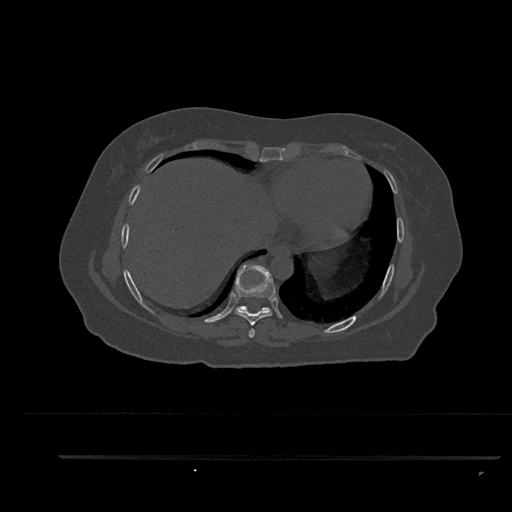
CT including the spine, one axial slice; position 449 of 797 along the scan axis; reconstruction kernel Br40s/3; 120 kVp; bone window (W 1800 / L 400 HU); 0.5 mm slice thickness; 512 × 512 image matrix. Patient: female, 44 years. Case-level facts recorded for this patient, not image findings: primary cancer: renal; vertebrae with lytic lesions (as recorded): L1.
Outlined on this slice (semi-automatic segmentation, software-assisted and operator-edited):
- T7 vertebra: bounding box <249,328,255,338> (left, top, right, bottom; pixels)
- T8 vertebra: <234,263,276,326>
- T9 vertebra: <235,306,269,313>